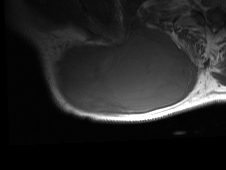
MRI of an extremity soft-tissue mass, one axial slice. Position 47 of 81 along the scan axis. MR volume resampled by the dataset authors to the PET/CT grid (not the native acquisition matrix). 226 × 170 image matrix, field of view 221 × 166 mm. Male patient. From the clinical record (not read from this slice): histological type: pleiomorphic spindle cell undifferentiated; grade: high; site of the primary tumour: right parascapusular.
Outlined on this slice (expert contour drawn on MRI and transferred to this co-registered scan by the dataset authors):
- gross tumour volume including surrounding oedema: box from (x=51, y=26) to (x=196, y=117) px
- gross tumour volume (mass): (x=53, y=29)–(x=189, y=114)